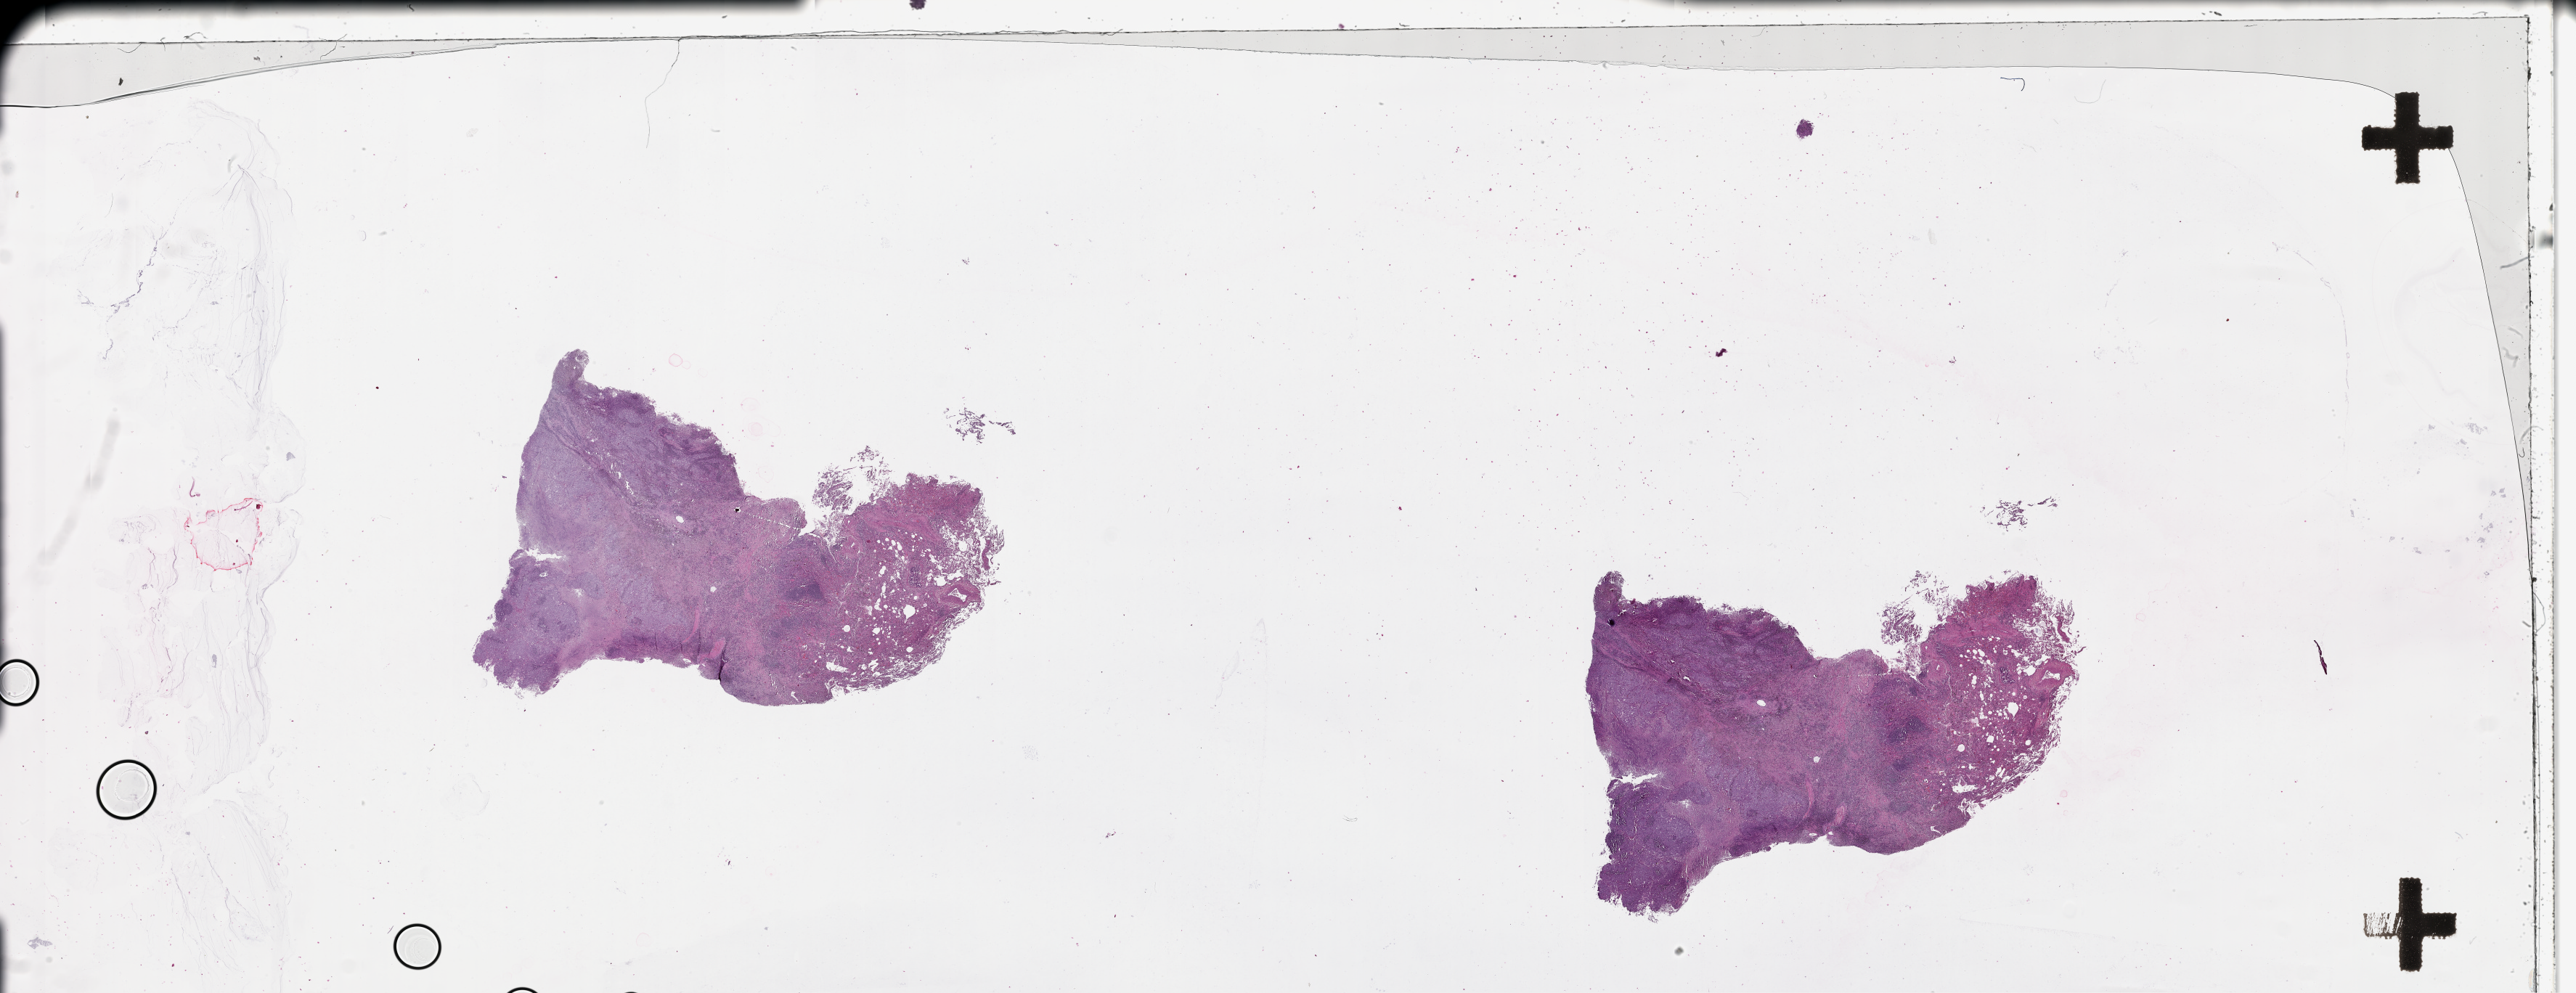
Whole-slide histology image, H&E, whole scanned area (about 57.1 x 22.0 mm, from a 20x scan) shown as a low-resolution overview, lung, tumour tissue. 71-year-old male patient.
Patient diagnosis (cohort enrolment): squamous cell carcinoma (lung).